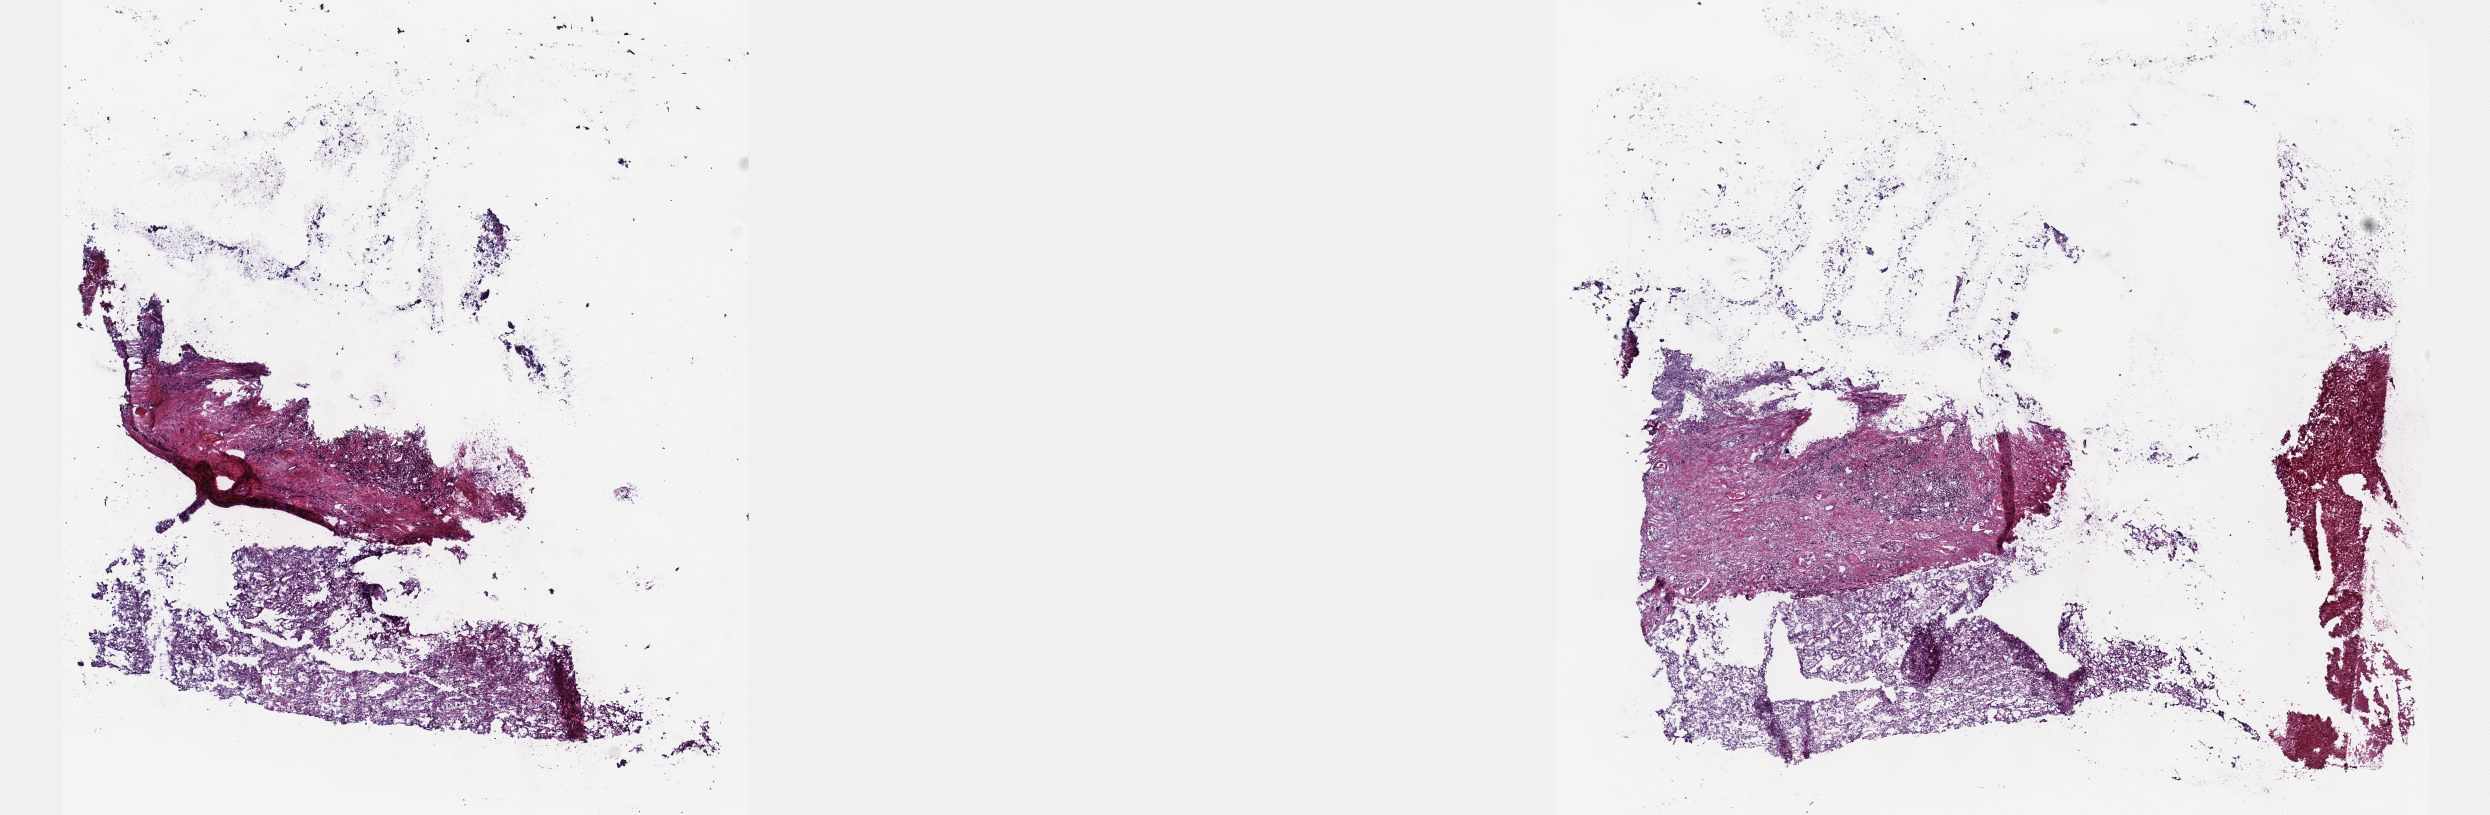
Digitized Hematoxylin and eosin (H&E) stained tissue section (whole slide), whole scanned area (about 20.1 x 6.6 mm) shown as a low-resolution overview; frozen section from the top of the tissue portion; primary tumour sample from the kidney. Male, age 79 years at initial diagnosis. Composition of this section per pathologist review: tumour cells 55%, tumour nuclei 70%, normal cells 15%, stromal cells 30%, necrosis 0%. Inflammatory infiltration, as recorded: lymphocyte infiltration 0%, monocyte infiltration 0%, neutrophil infiltration 0%.
Laterality: left. AJCC pathologic stage: III. Pathologic diagnosis: Papillary adenocarcinoma, NOS.